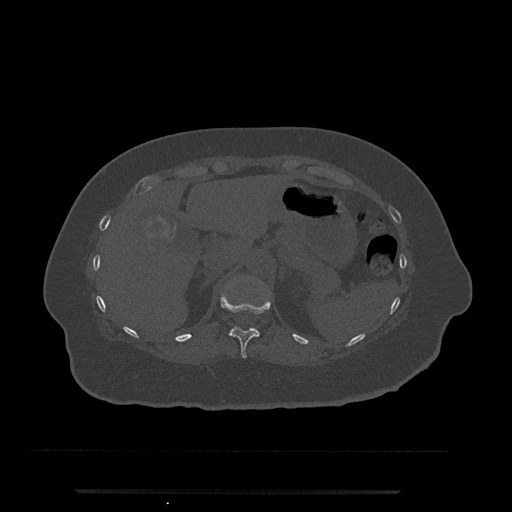
CT including the spine, one axial slice. Slice 212 of 797 in the series (ordered by position). 120 kVp. Bone window (W 1800 / L 400 HU). 0.5 mm slice thickness. 512 × 512 image matrix, field of view 440 × 440 mm. Female patient, age 51 years. From the clinical record (not read from this slice): primary cancer: neuro.
Outlined on this slice (semi-automatic segmentation, software-assisted and operator-edited):
- T11 vertebra: bounding box <221,292,271,358> (left, top, right, bottom; pixels)